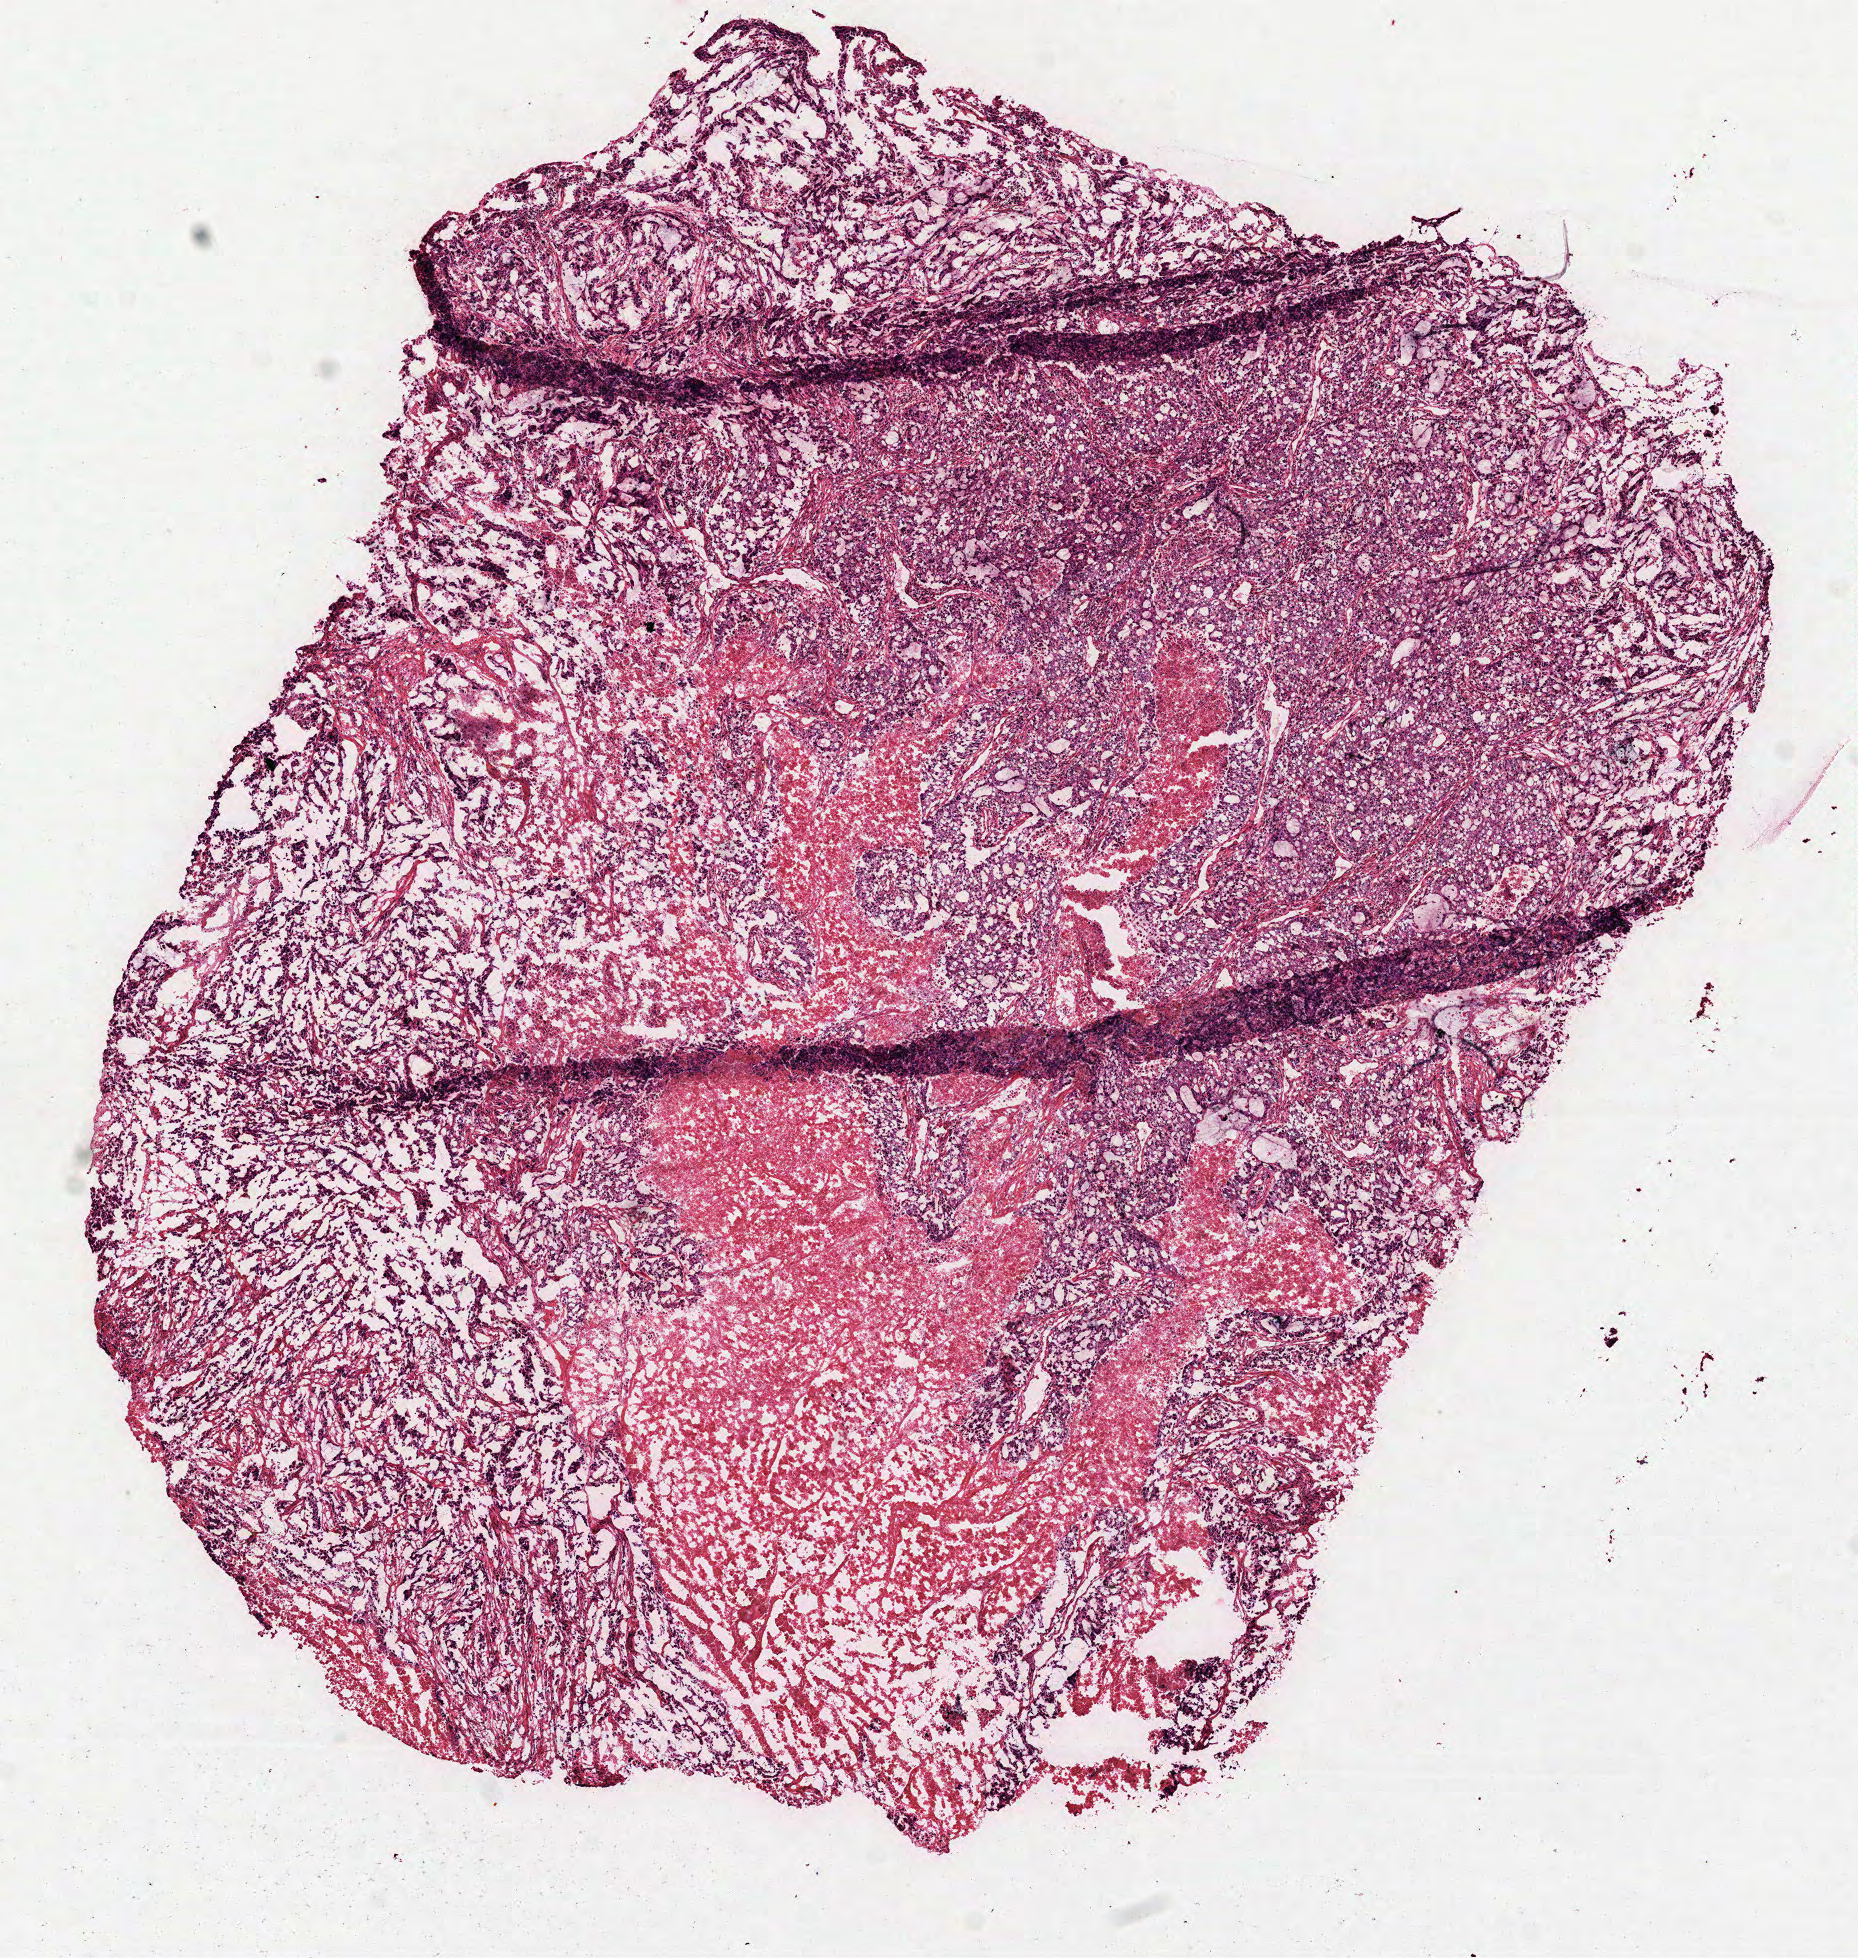
Whole-slide histology image, H&E — low-resolution overview of the scanned area, about 7.5 x 7.9 mm; frozen section from the top of the tissue portion; primary tumour sample from the lung. Patient: male, age at initial diagnosis 71 years. Pathologist review of this section (percent, as recorded): tumour cells 75%, tumour nuclei 70%, normal cells 0%, stromal cells 5%, necrosis 20%.
• laterality: right
• diagnosis: Adenocarcinoma, NOS (lower lobe, lung)
• AJCC pathologic stage: IIA